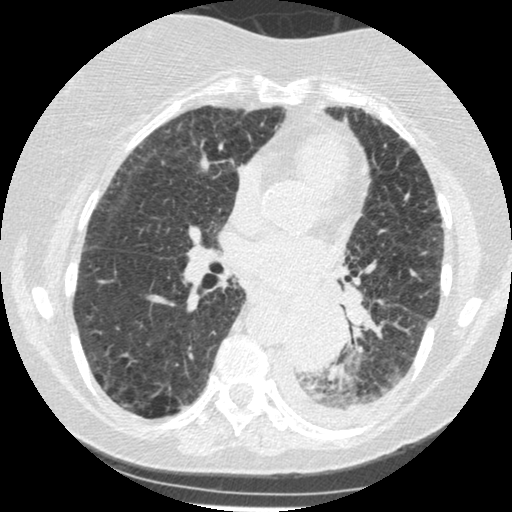
Low-dose screening chest CT, one axial slice; slice 121 of 341 in the series (ordered by position); 120 kVp; lung window (W 1500 / L -600 HU); 1.25 mm slice thickness; 512 × 512 image matrix, field of view 310 × 310 mm.
Structures marked on this image (expert manual segmentation):
- lesion 1 (tumor, lower lobe of left lung): bounding box <284,301,345,373> (left, top, right, bottom; pixels)